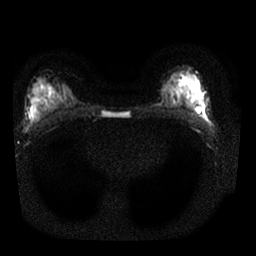
Breast MRI, one axial slice. Position 12 of 25 along the scan axis. Diffusion-weighted series; image 2 of 4 stored at this slice position (different b-values; order by instance number). 1.5 T. 256 × 256 image matrix. Female patient.
Annotated regions visible in this slice (outlined manually by an expert reader):
- tumour on diffusion-weighted imaging: bounding box <192,103,196,109> (left, top, right, bottom; pixels)